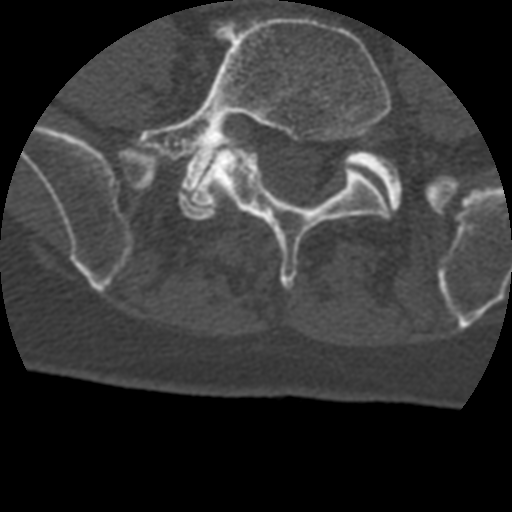
CT including the spine, one axial slice. Slice 40 of 399 in the series (ordered by position). 120 kVp. Bone window (W 1800 / L 400 HU). 1.25 mm slice thickness. 512 × 512 image matrix, field of view 160 × 160 mm. Patient age 69 years. Case-level facts recorded for this patient, not image findings: primary cancer: prostate.
Structures marked on this image (semi-automatic segmentation, software-assisted and operator-edited):
- L4 vertebra: bounding box (x1, y1, x2, y2) in pixels: (216, 191, 227, 201)
- L5 vertebra: (132, 17, 392, 290)